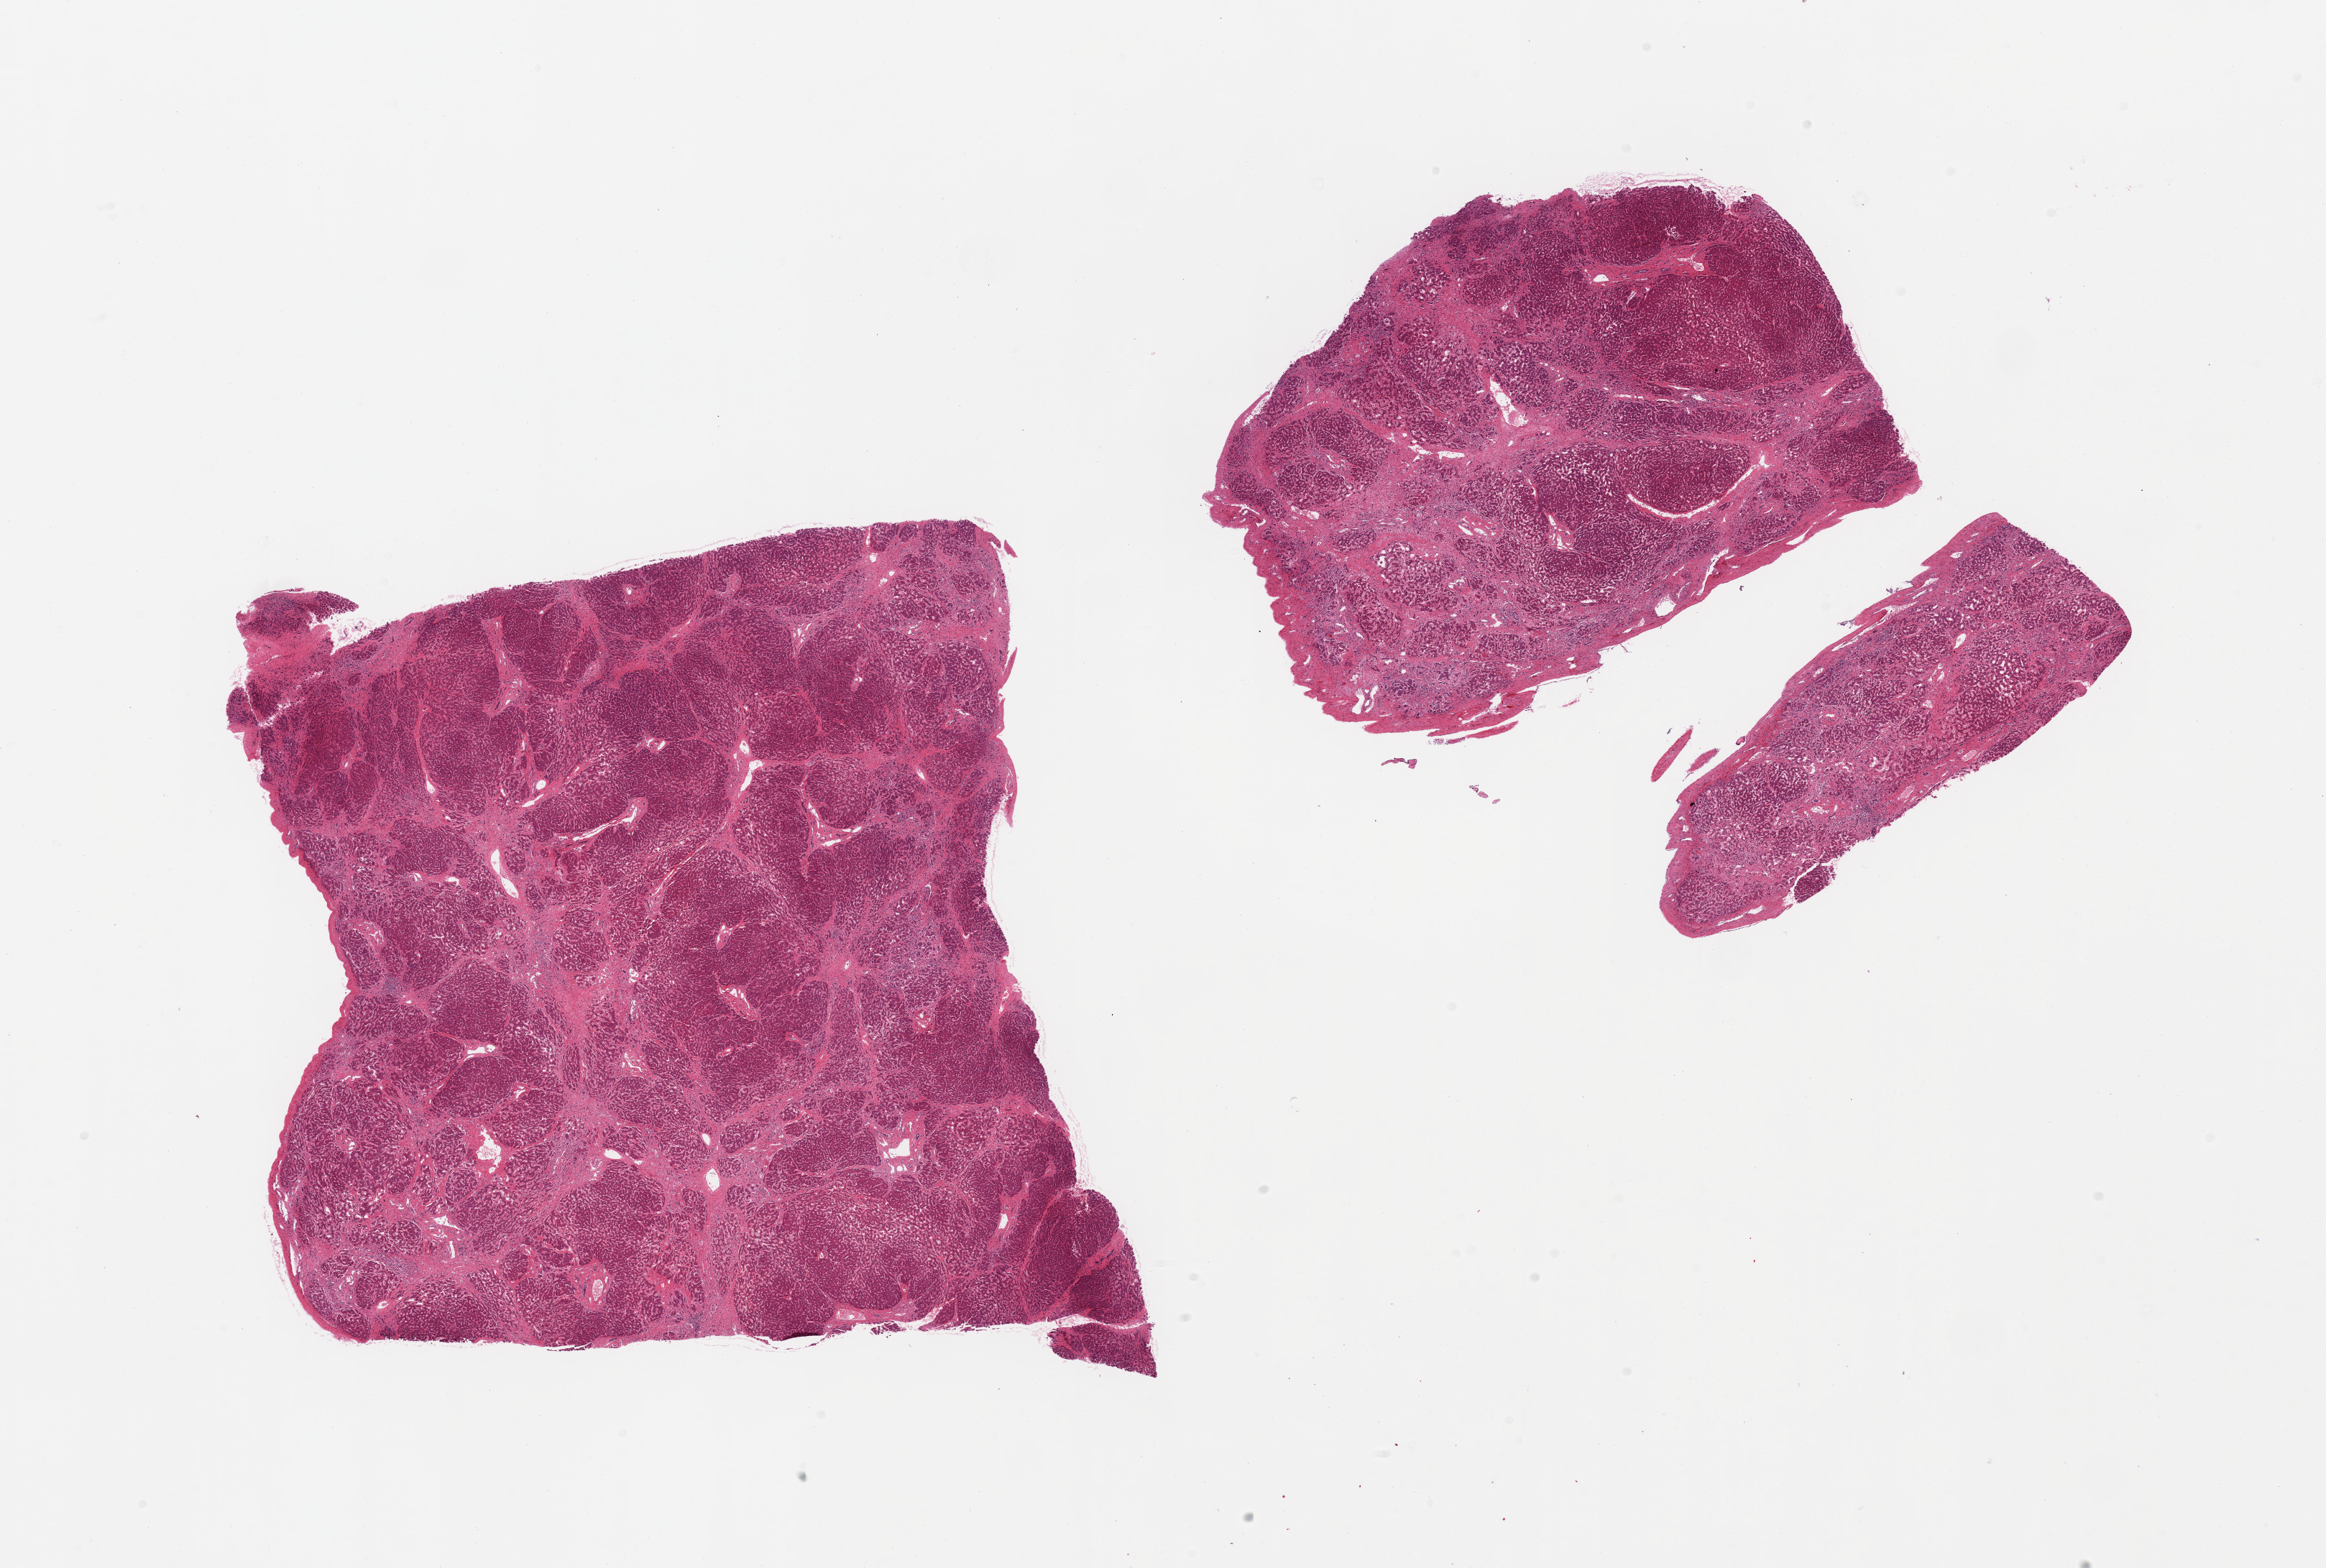
Digitized H&E-stained section — whole scanned area (about 25.6 x 17.3 mm) shown as a low-resolution overview; PAXgene-fixed paraffin-embedded (PFPE) section; target tissue: liver; donor tissue sample. Donor sex: male.
• pathologist's review note for this sample: 3 pieces; capsule included; advanced cirrhosis